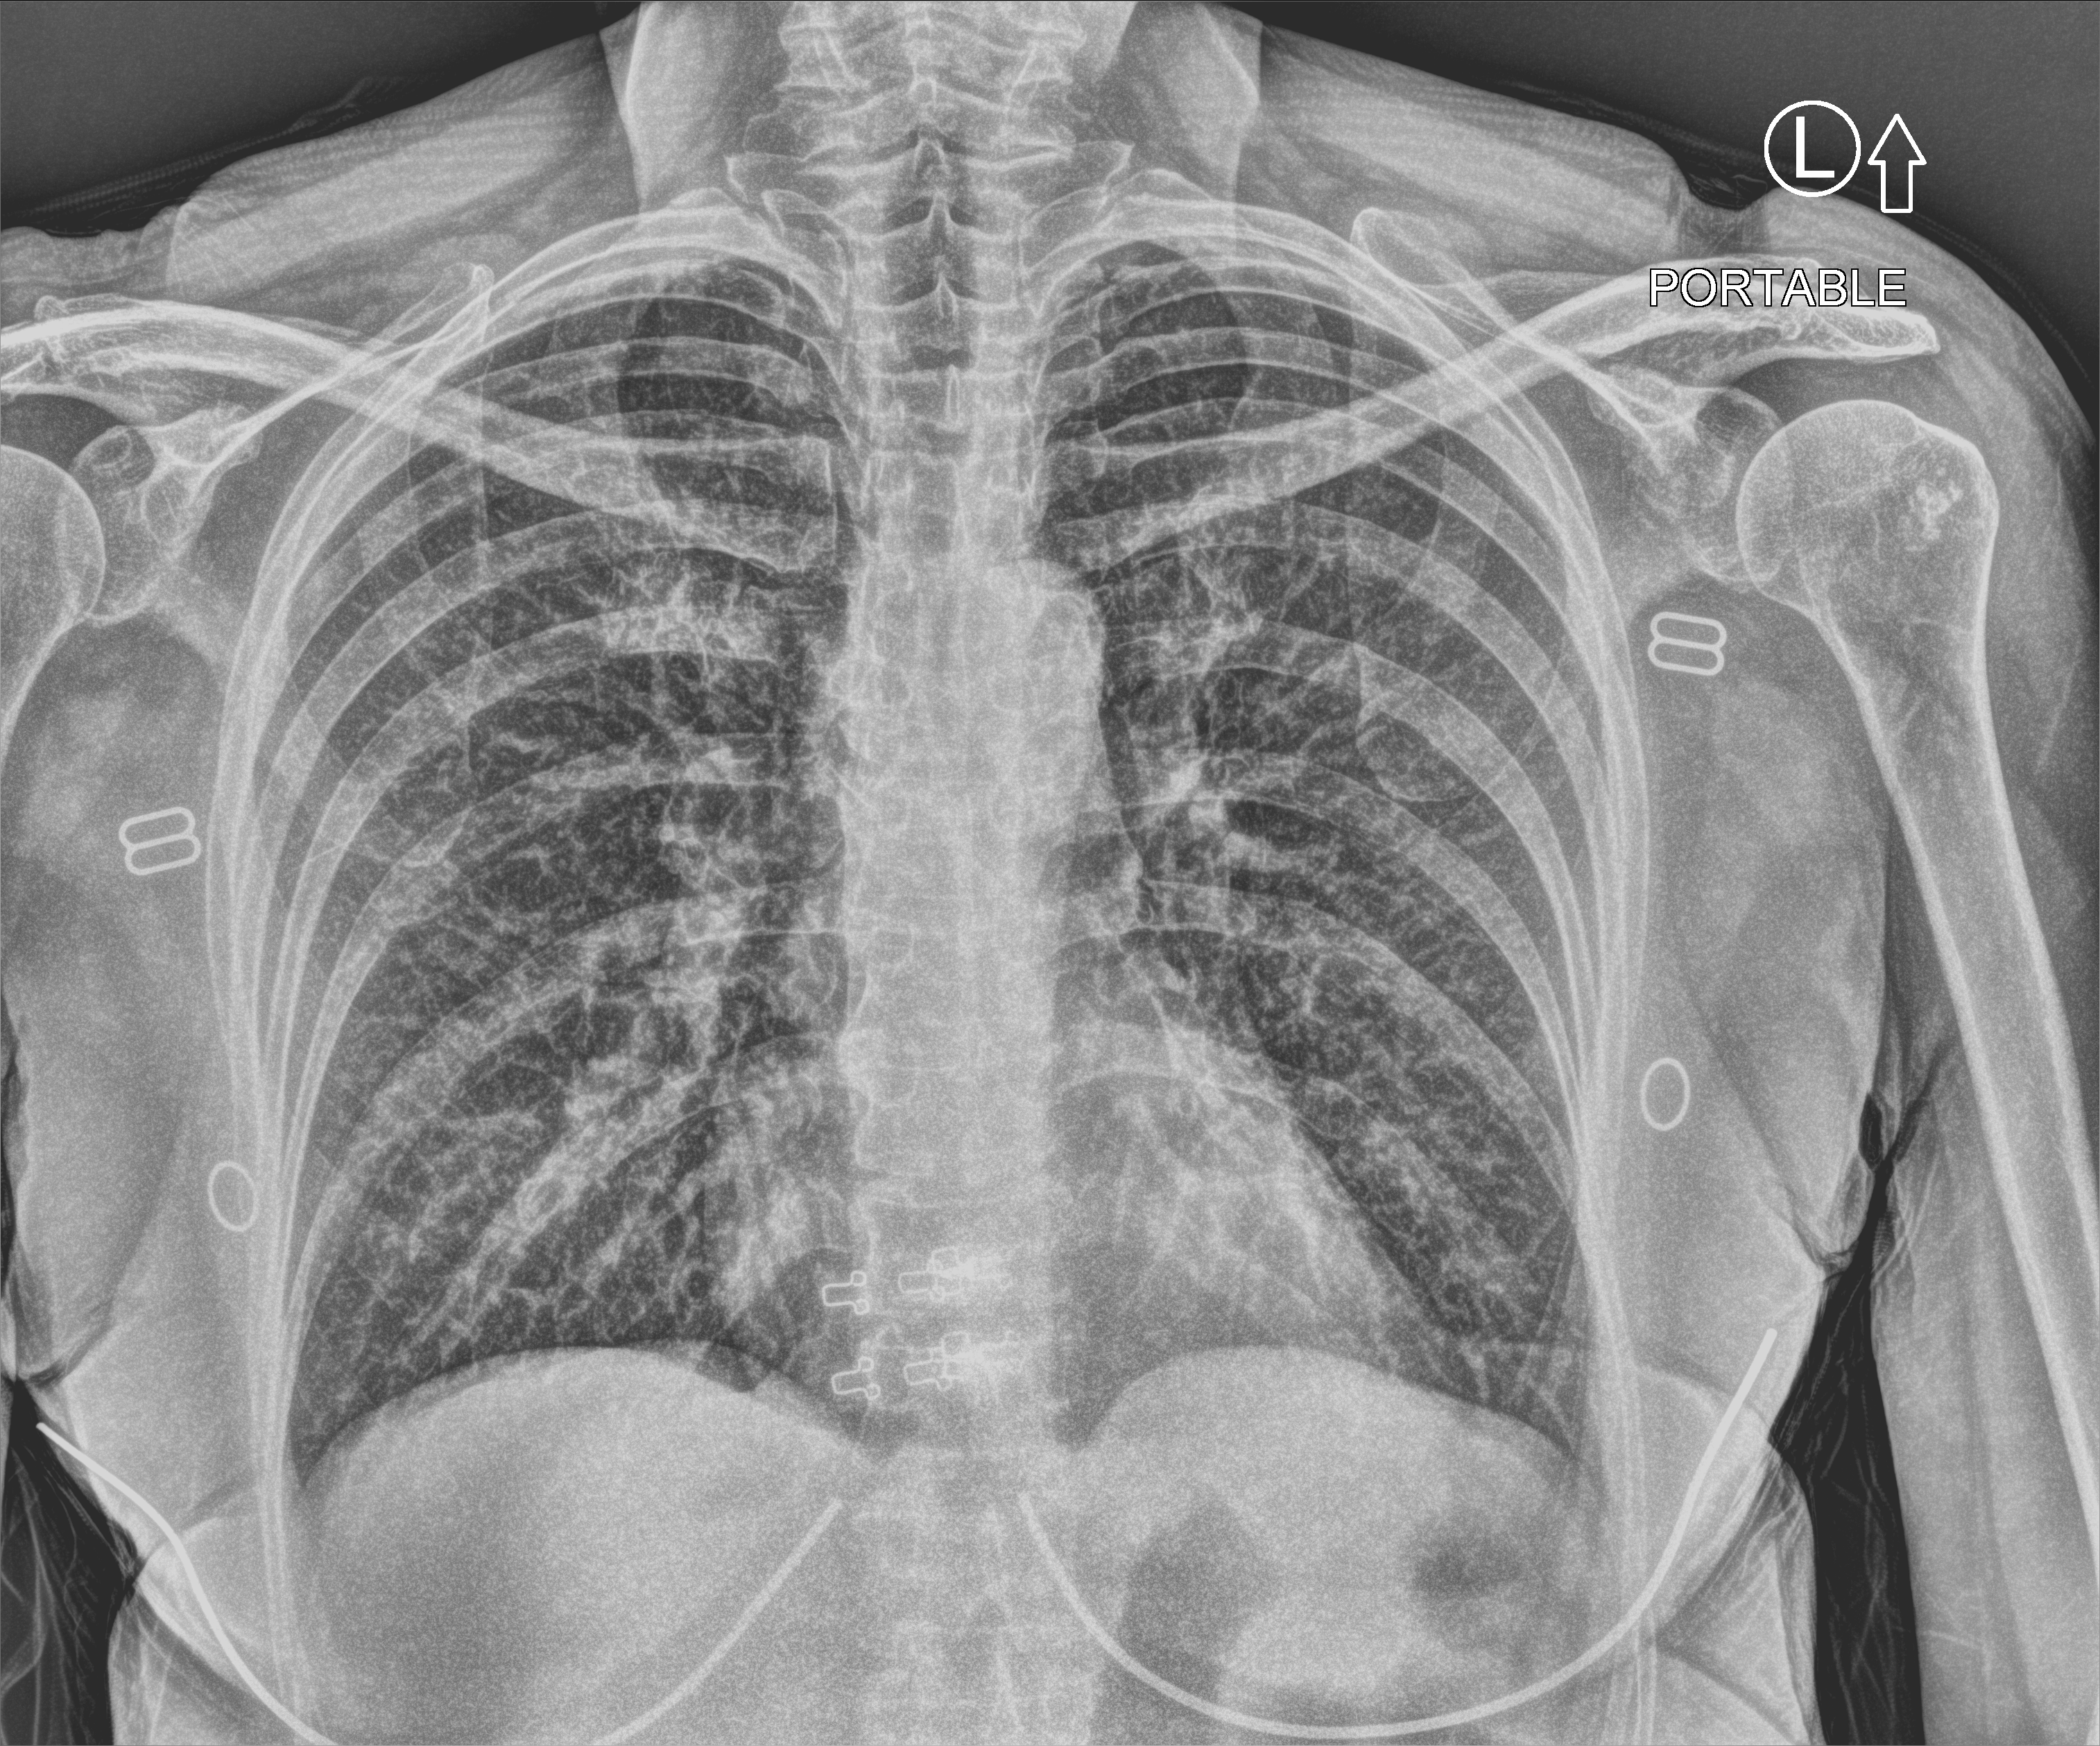
Bedside chest radiograph (computed radiography), anteroposterior (AP) projection. Female patient hospitalised with COVID-19, age 60–74 years.
From the hospital-stay record, not from the radiograph (when in the stay this image was taken is not recorded): admitted to intensive care during this hospital stay: no; length of hospital stay: 1 day; mechanically ventilated during this hospital stay: no.